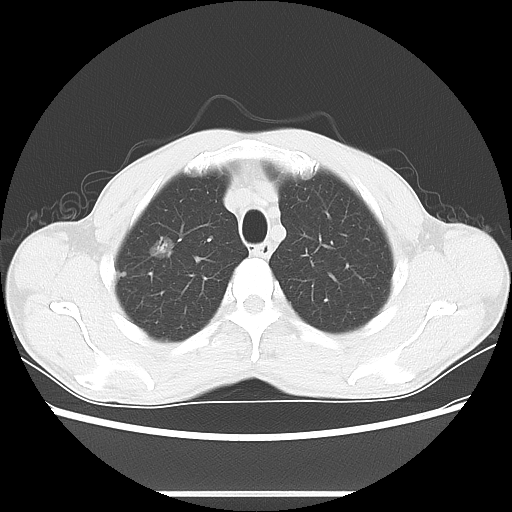
Chest CT, one axial slice; position 62 of 76 along the scan axis; reconstruction kernel LUNG; 100 kVp; lung window (W 1500 / L -600 HU); 512 × 512 image matrix. Patient: male, 54 years. From the clinical record (not read from this slice): clinical TNM (as recorded): T1a N0 M0.
Annotated regions visible in this slice (rectangle marked by the reading radiologist):
- lung tumour (recorded histology: adenocarcinoma): bounding box <149,227,179,271> (left, top, right, bottom; pixels)